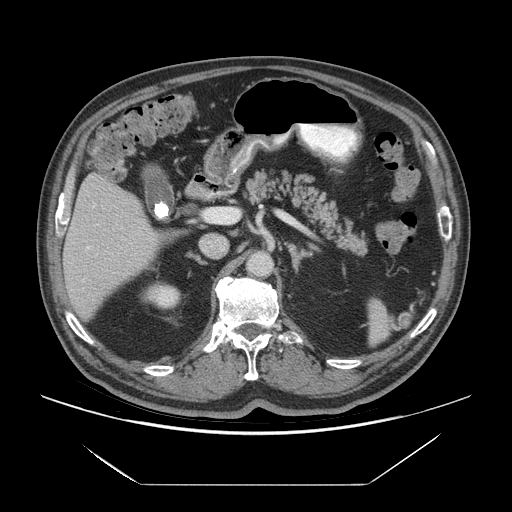
Contrast-enhanced abdominal CT (liver protocol), one axial slice; position 33 of 75 along the scan axis; reconstruction kernel STANDARD; 140 kVp; soft-tissue window (W 400 / L 40 HU); 512 × 512 image matrix, field of view 420 × 420 mm. From the clinical record (not read from this slice): diagnosis: hepatocellular carcinoma (patient treated with transarterial chemoembolisation; whether this scan precedes or follows treatment is not stated here); TNM stage (as recorded): Stage-I; Child-Pugh class: A; tumour nodularity: uninodular; tumour size: 5.8 cm.
Annotated regions visible in this slice (semi-automatic segmentation, software-assisted and operator-edited):
- liver parenchyma outside the tumour (the mass and vessels are separate outlines, so this box may not span the whole liver): box from (x=62, y=172) to (x=158, y=318) px
- liver vessels: (x=87, y=203)–(x=95, y=249)